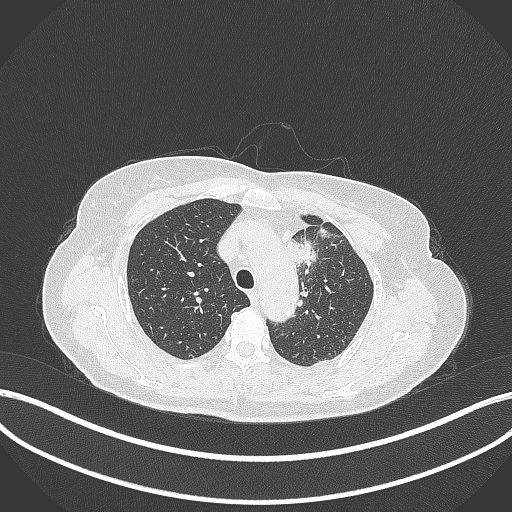
Chest CT, one axial slice. Slice 255 of 369 in the series (ordered by position). Reconstruction kernel B70f. 120 kVp. Lung window (W 1500 / L -600 HU). 512 × 512 image matrix. Patient: female, 65 years. From the clinical record (not read from this slice): clinical TNM (as recorded): T2a N0 M0.
Structures marked on this image (bounding box drawn by a radiologist):
- lung tumour (recorded histology: adenocarcinoma): box from (x=284, y=235) to (x=321, y=268) px